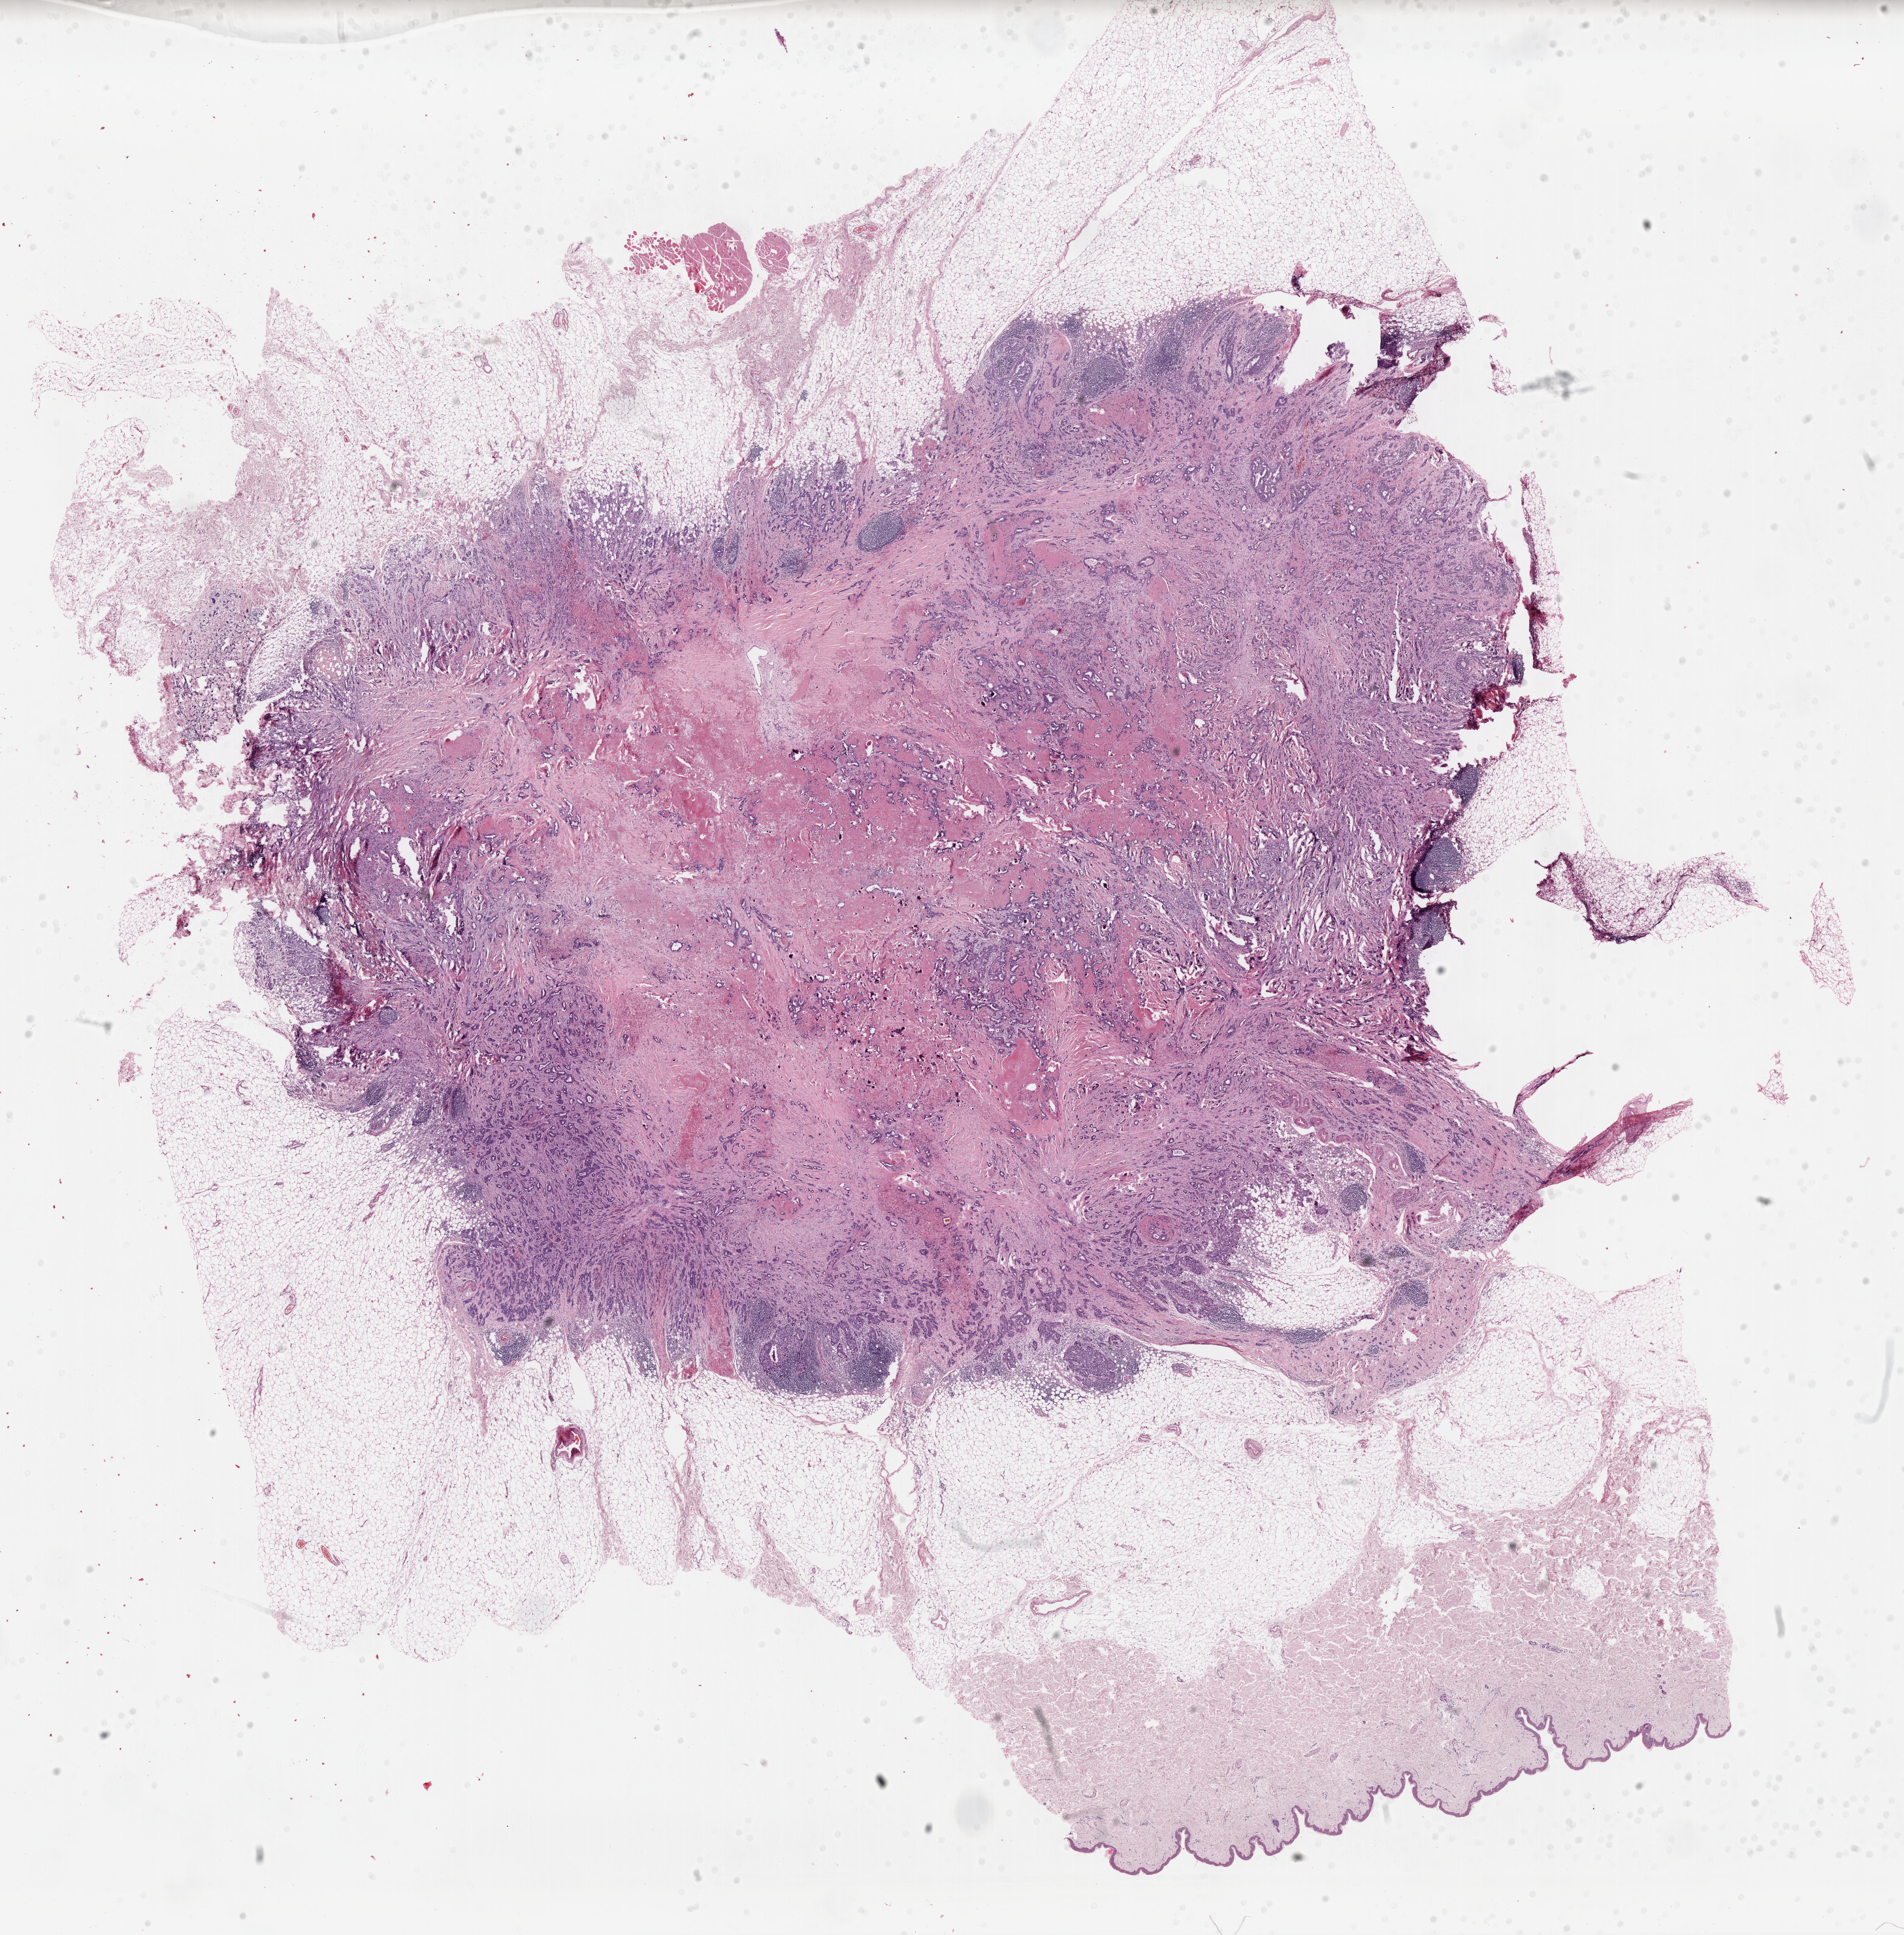
Whole-slide histology image, H&E — whole scanned area (about 23.0 x 23.4 mm, slide scanned at 40x) shown as a low-resolution overview, FFPE section, breast, primary tumour sample. Female patient; age at initial diagnosis 62 years.
TNM: T2 N1a M0. Laterality: right. AJCC pathologic stage: IIB (7th edition). Lymph nodes positive (case pathology): 1 of 10 examined. Histologic diagnosis: Infiltrating duct carcinoma, NOS.